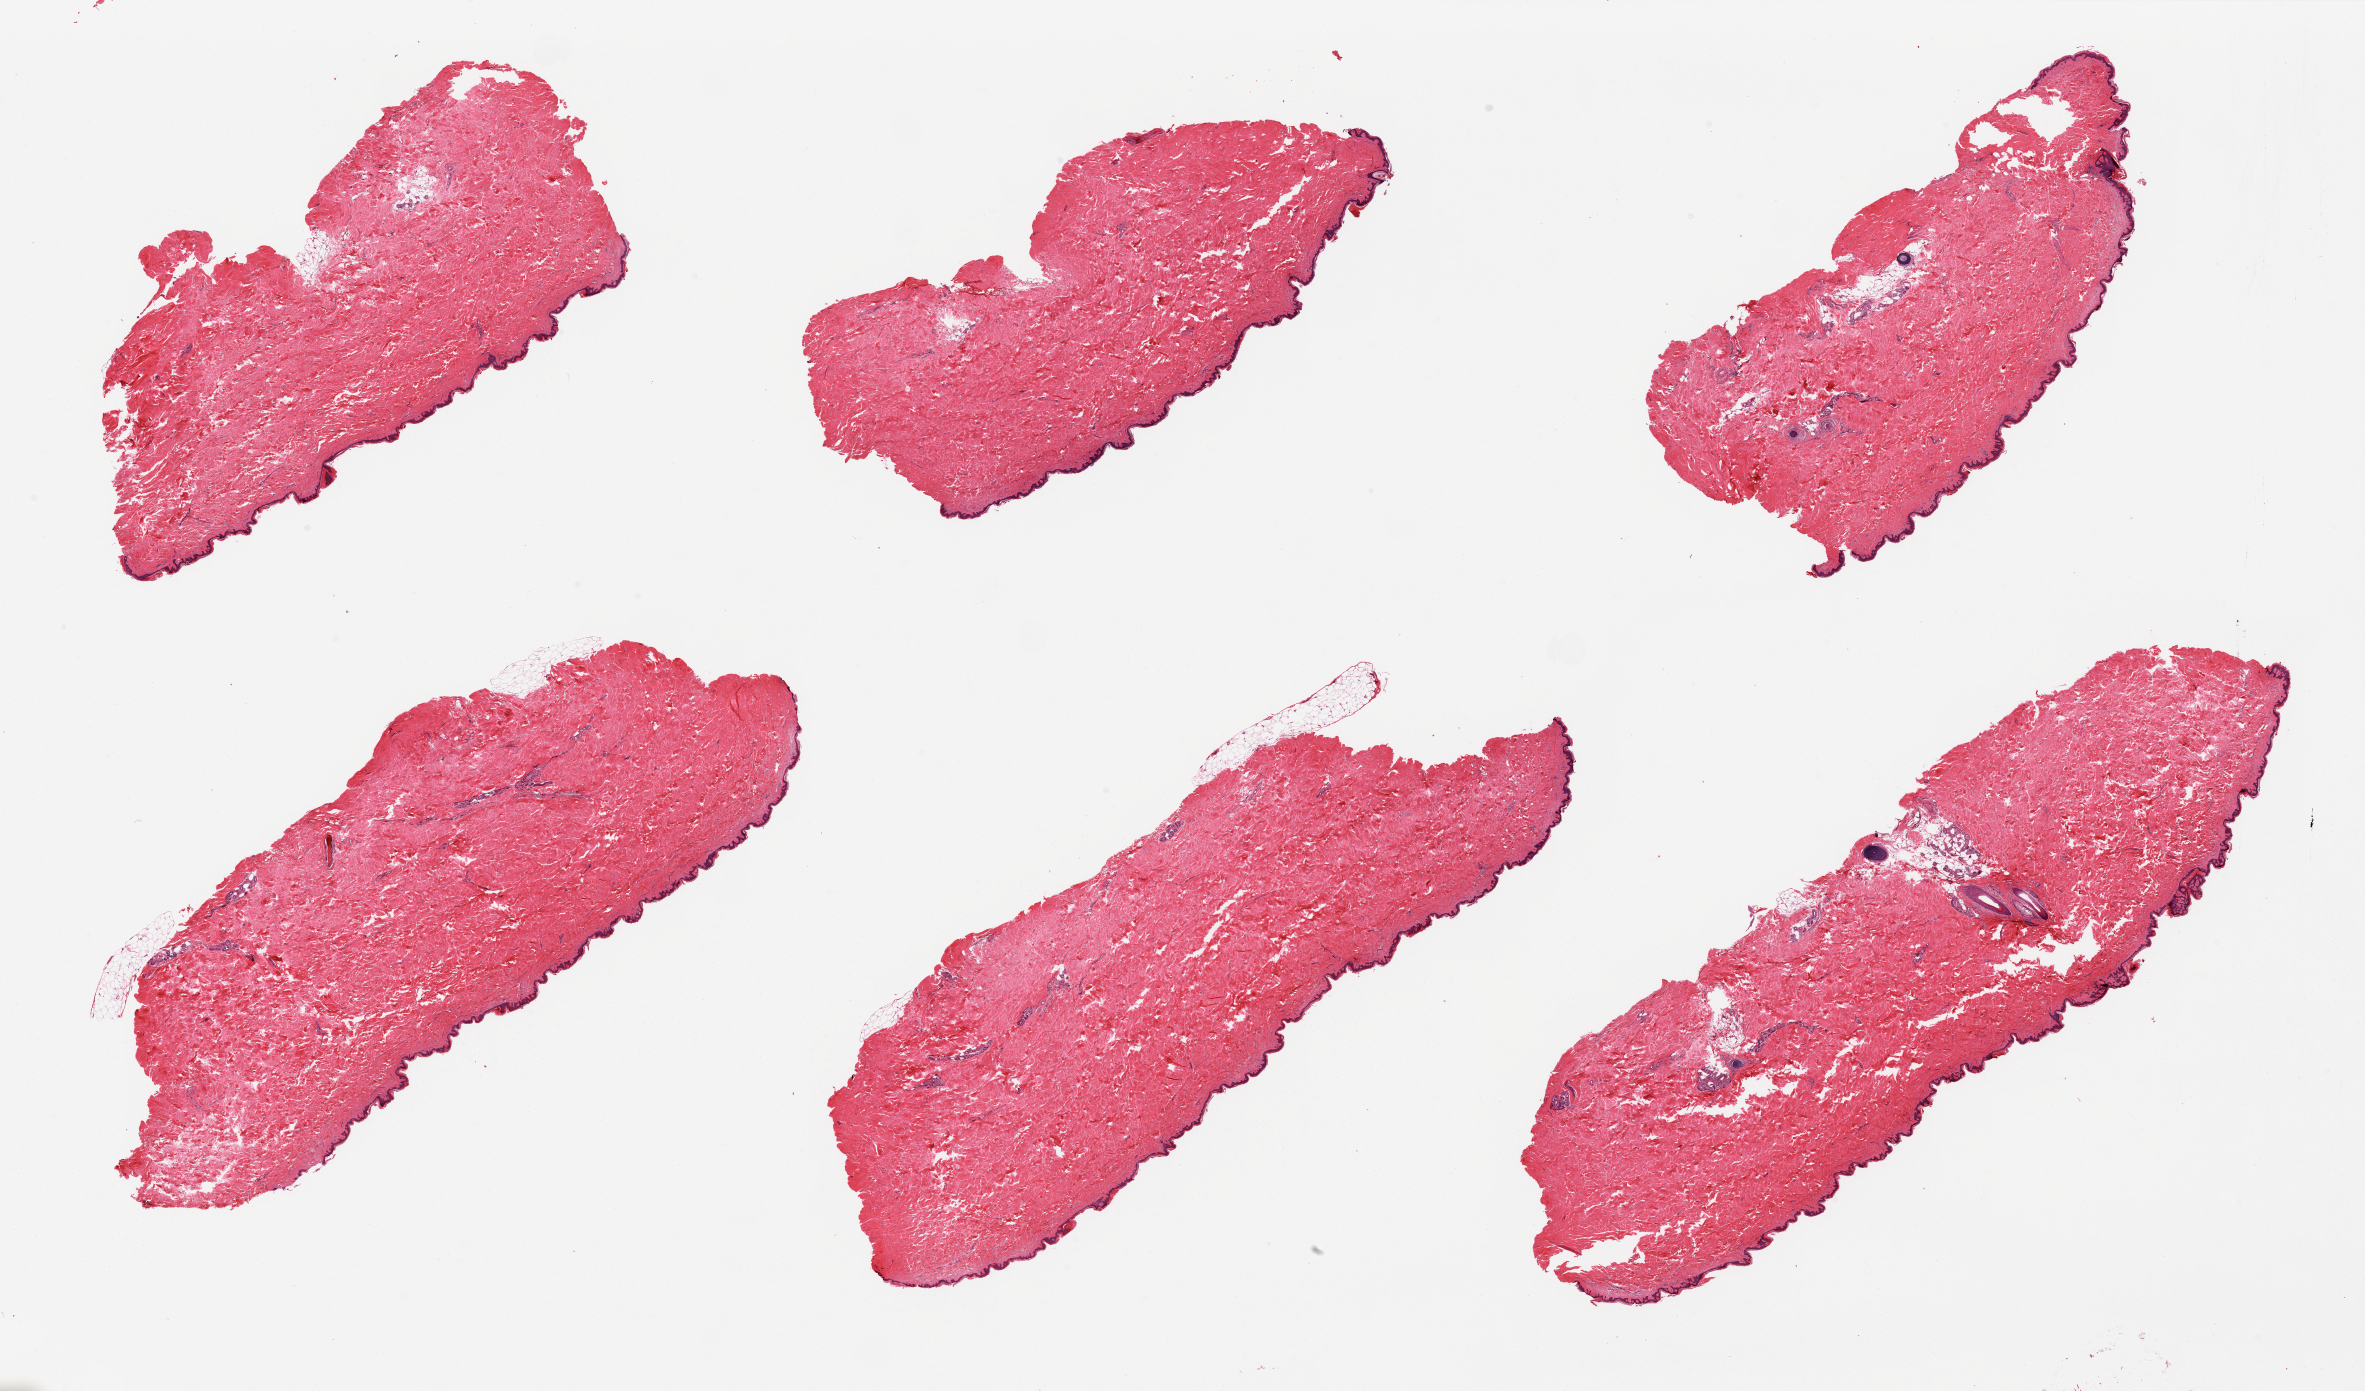
Digitized haematoxylin and eosin-stained section, brightfield, shown as a low-resolution overview of the whole scanned area (about 37.4 x 22.0 mm, from a 20x scan); PAXgene-fixed paraffin-embedded (PFPE) section; section of skin of suprapubic region (target tissue); tissue donor sample.
- review note (as recorded): 6 pieces, well trimmed